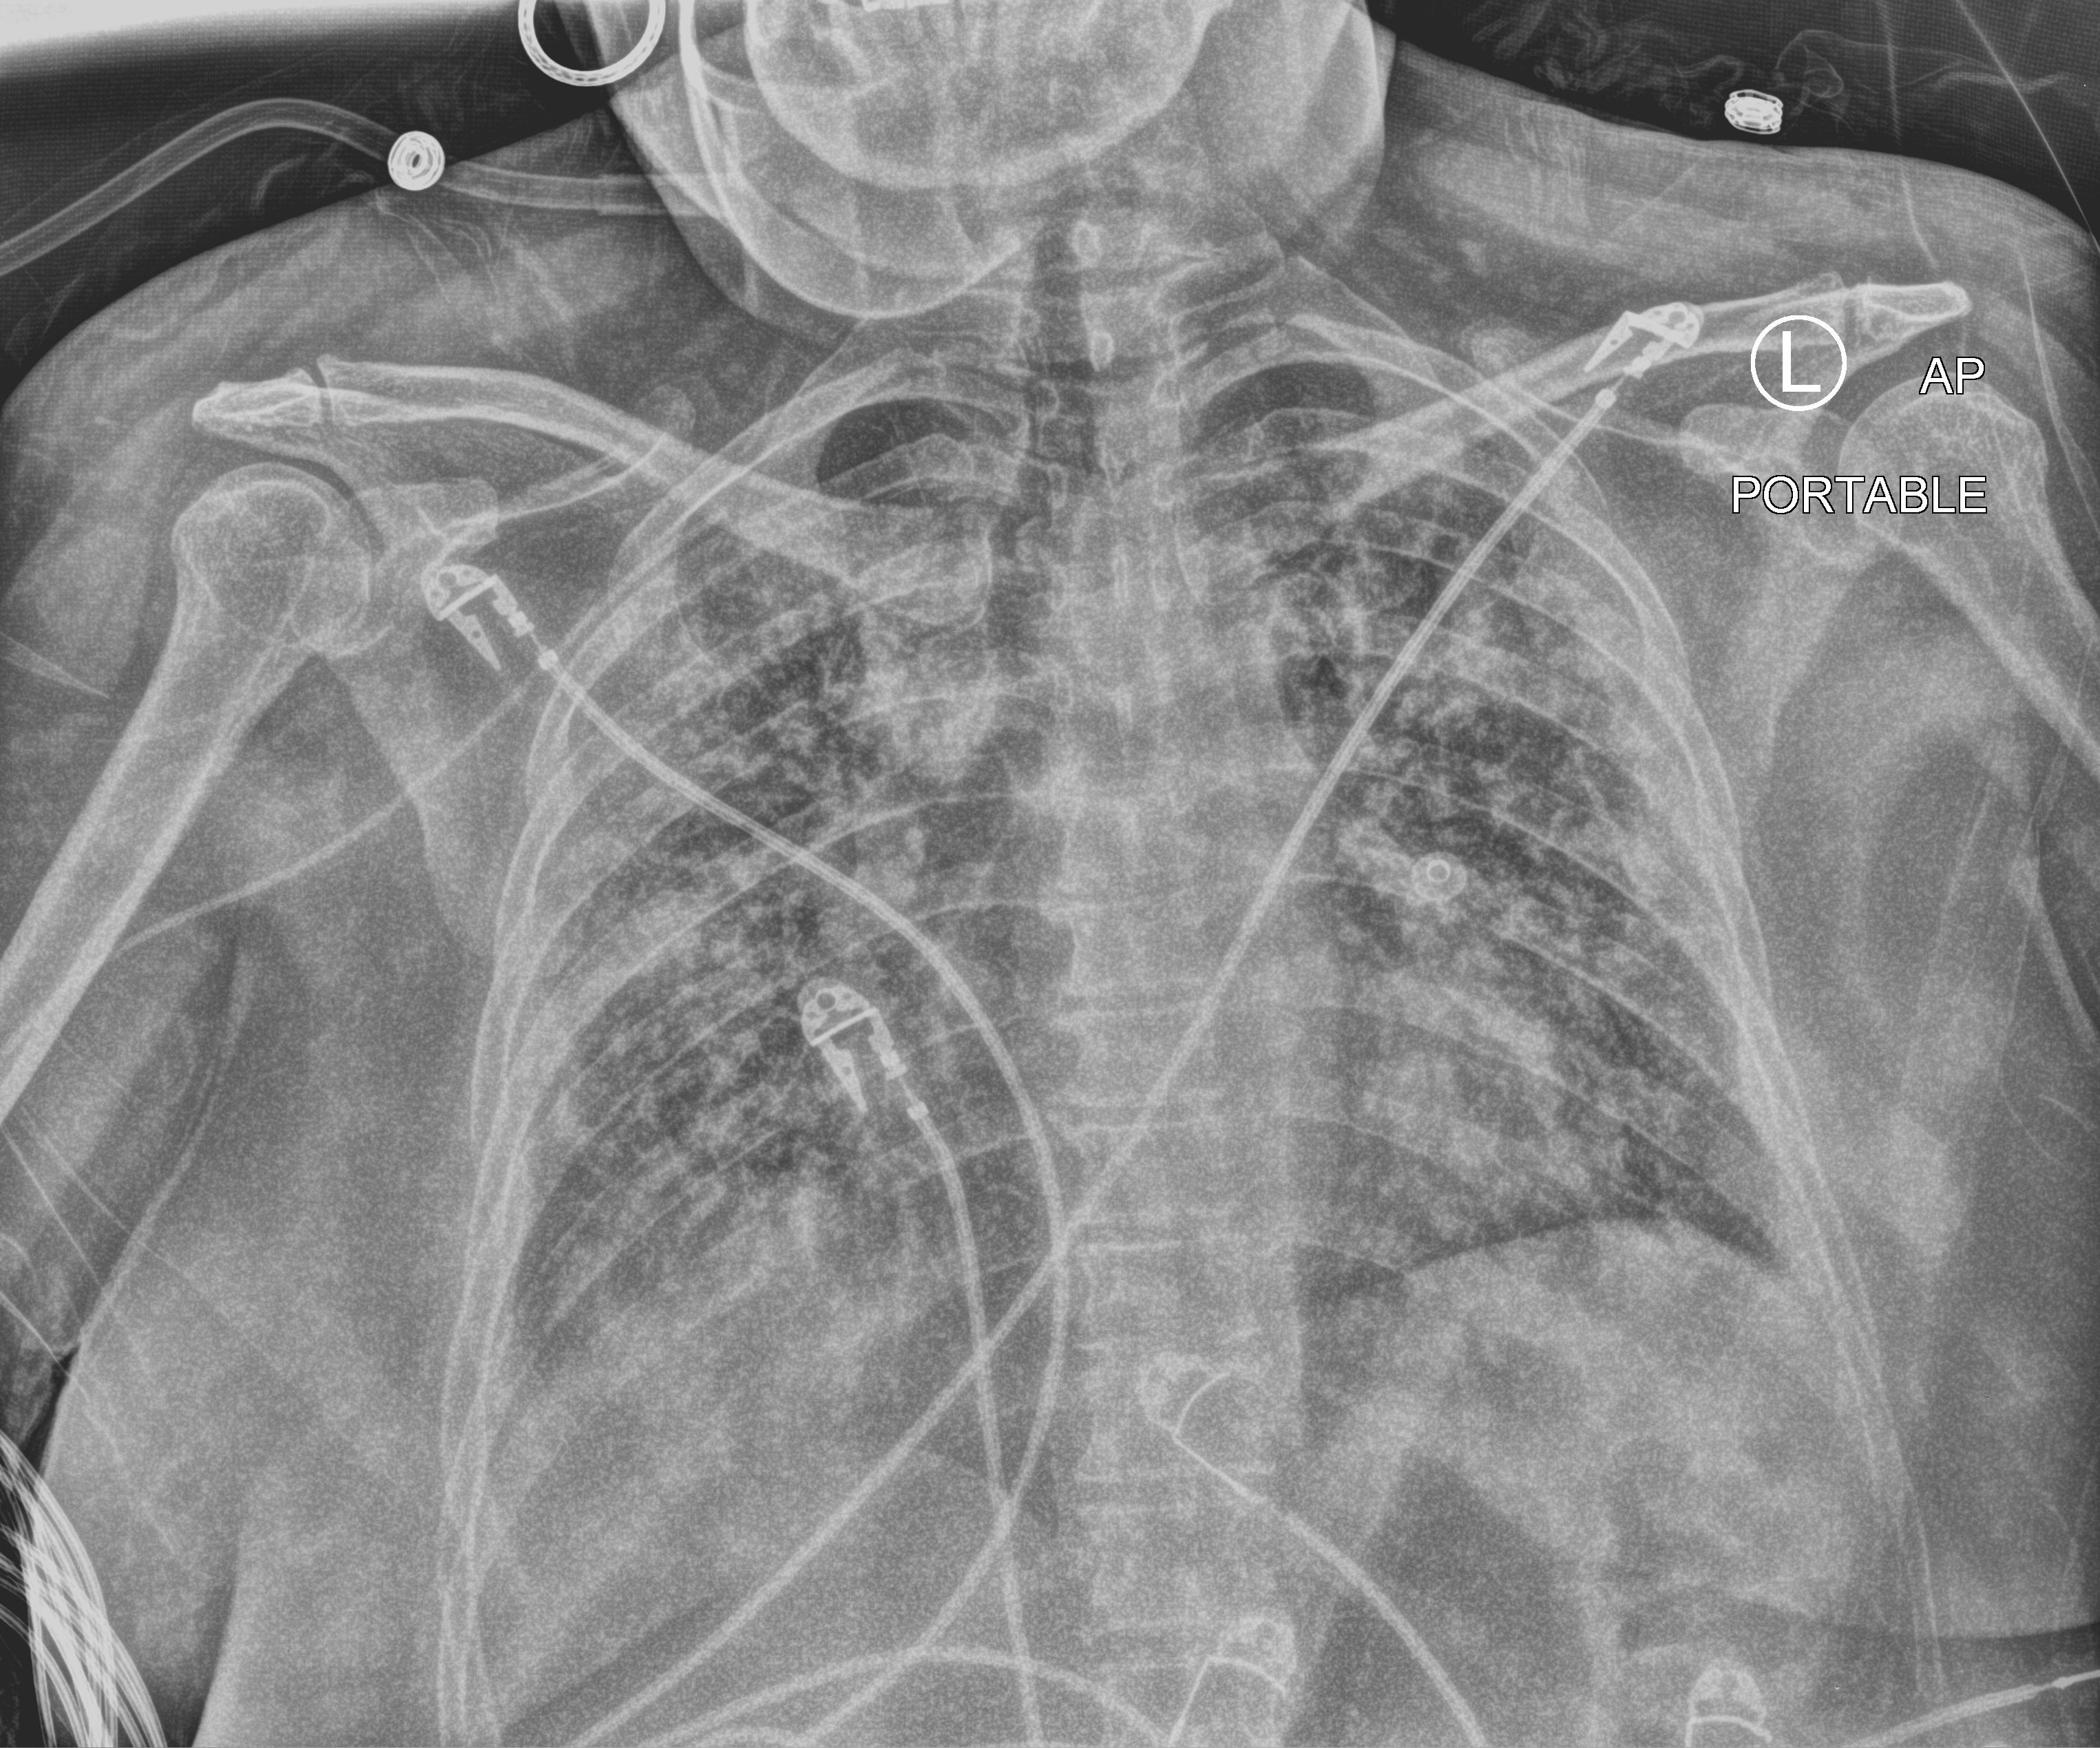
Portable chest radiograph; anteroposterior (AP) projection. Patient hospitalised with COVID-19; female, aged 18–59 years.
From the hospital-stay record, not from the radiograph (when in the stay this image was taken is not recorded):
- admitted to intensive care during this hospital stay: no
- mechanically ventilated during this hospital stay: no